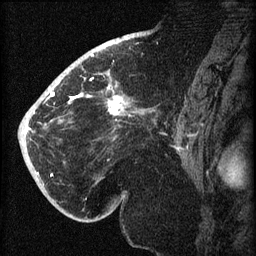
Breast MRI (dynamic contrast-enhanced), one sagittal slice; position 41 of 60 along the scan axis; dynamic contrast-enhanced series, image 2 of 3 at this slice position (ordered by acquisition); 1.5 T; TE 4.2 ms, TR 8.2 ms; 256 × 256 image matrix, field of view 180 × 180 mm. Patient: female, 71 years.
Outlined on this slice (semi-automatic segmentation, software-assisted and operator-edited):
- analysis volume of interest (the breast-tissue region the enhancement analysis was run in; not a lesion): box from (x=40, y=72) to (x=148, y=196) px
- tumour enhancement mask (voxels above the 70 % enhancement threshold inside the analysis volume of interest): (x=44, y=78)–(x=126, y=122)